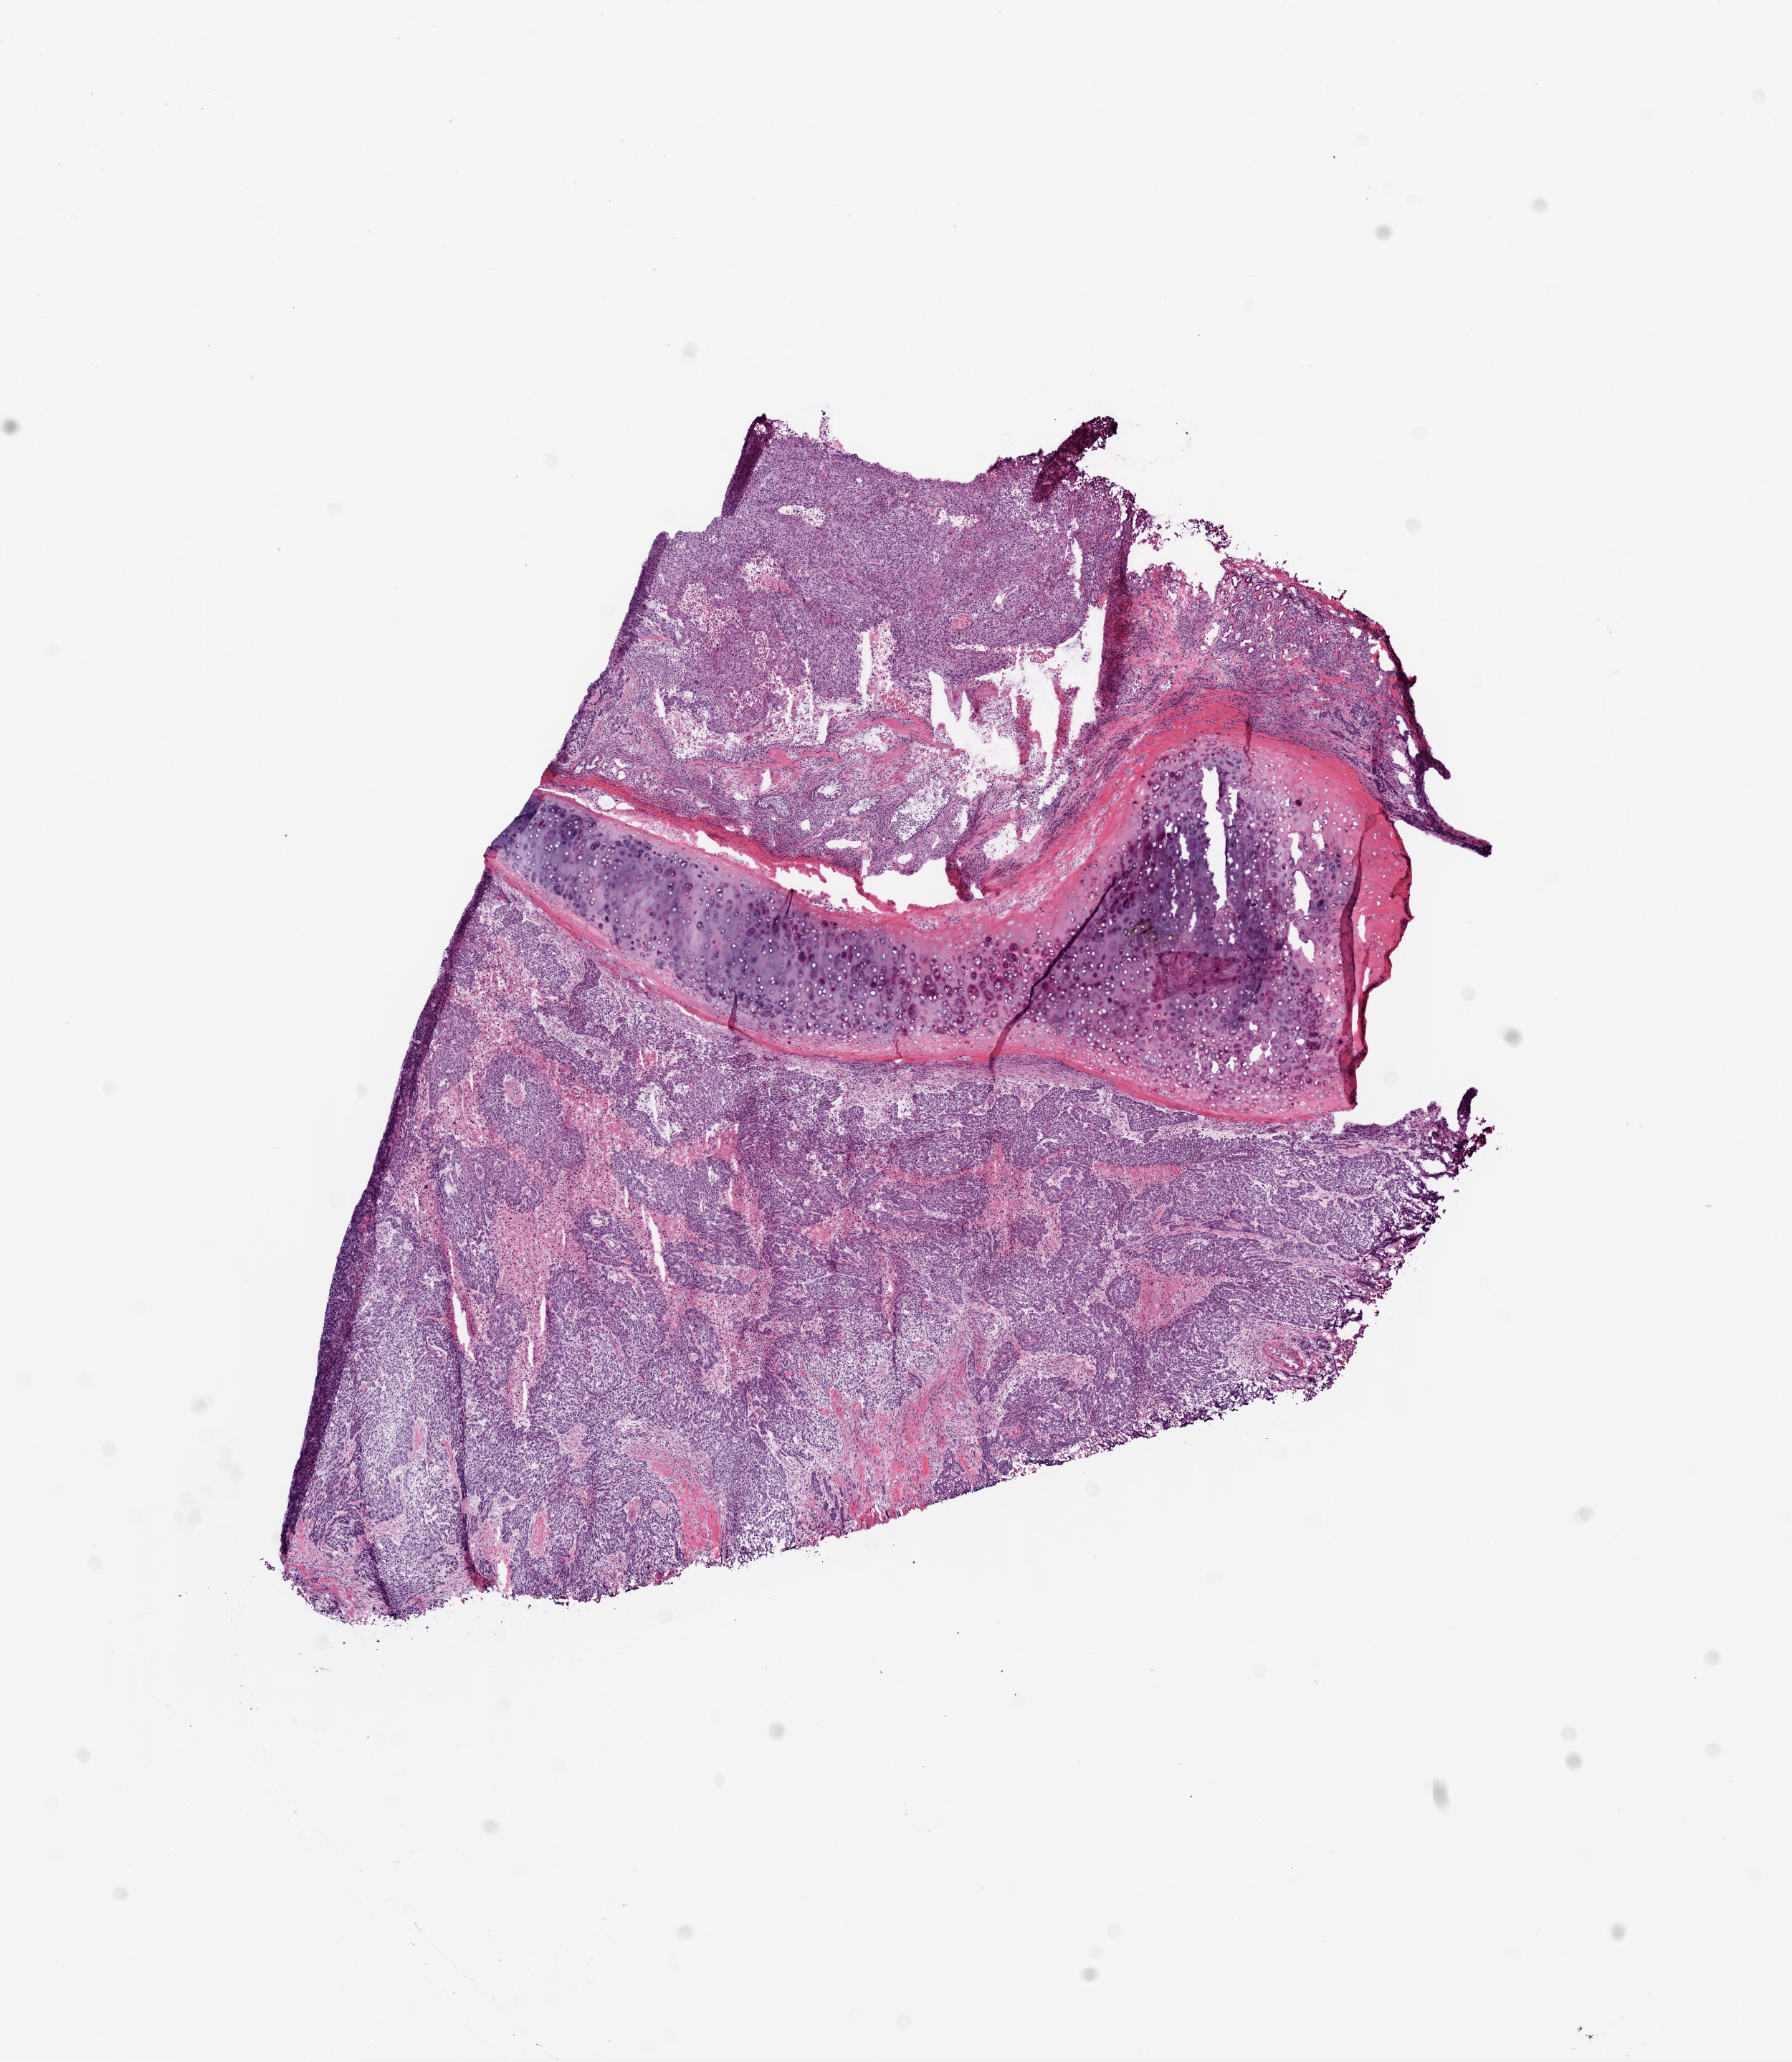
Whole-slide histology image, Hematoxylin and eosin (H&E) stained — a low-resolution overview of the entire scanned area, about 10.0 x 11.5 mm (acquisition: 20x scan). Frozen section from the bottom of the tissue portion. Sample: primary tumour, lung. Male, age 66 years at initial diagnosis. Pathologist review of this section (percent, as recorded): tumour cells 70%, tumour nuclei 85%, normal cells 15%, stromal cells 5%, necrosis 10%.
• AJCC pathologic stage: IIB
• diagnosis: Squamous cell carcinoma, NOS (upper lobe, lung)
• laterality: right